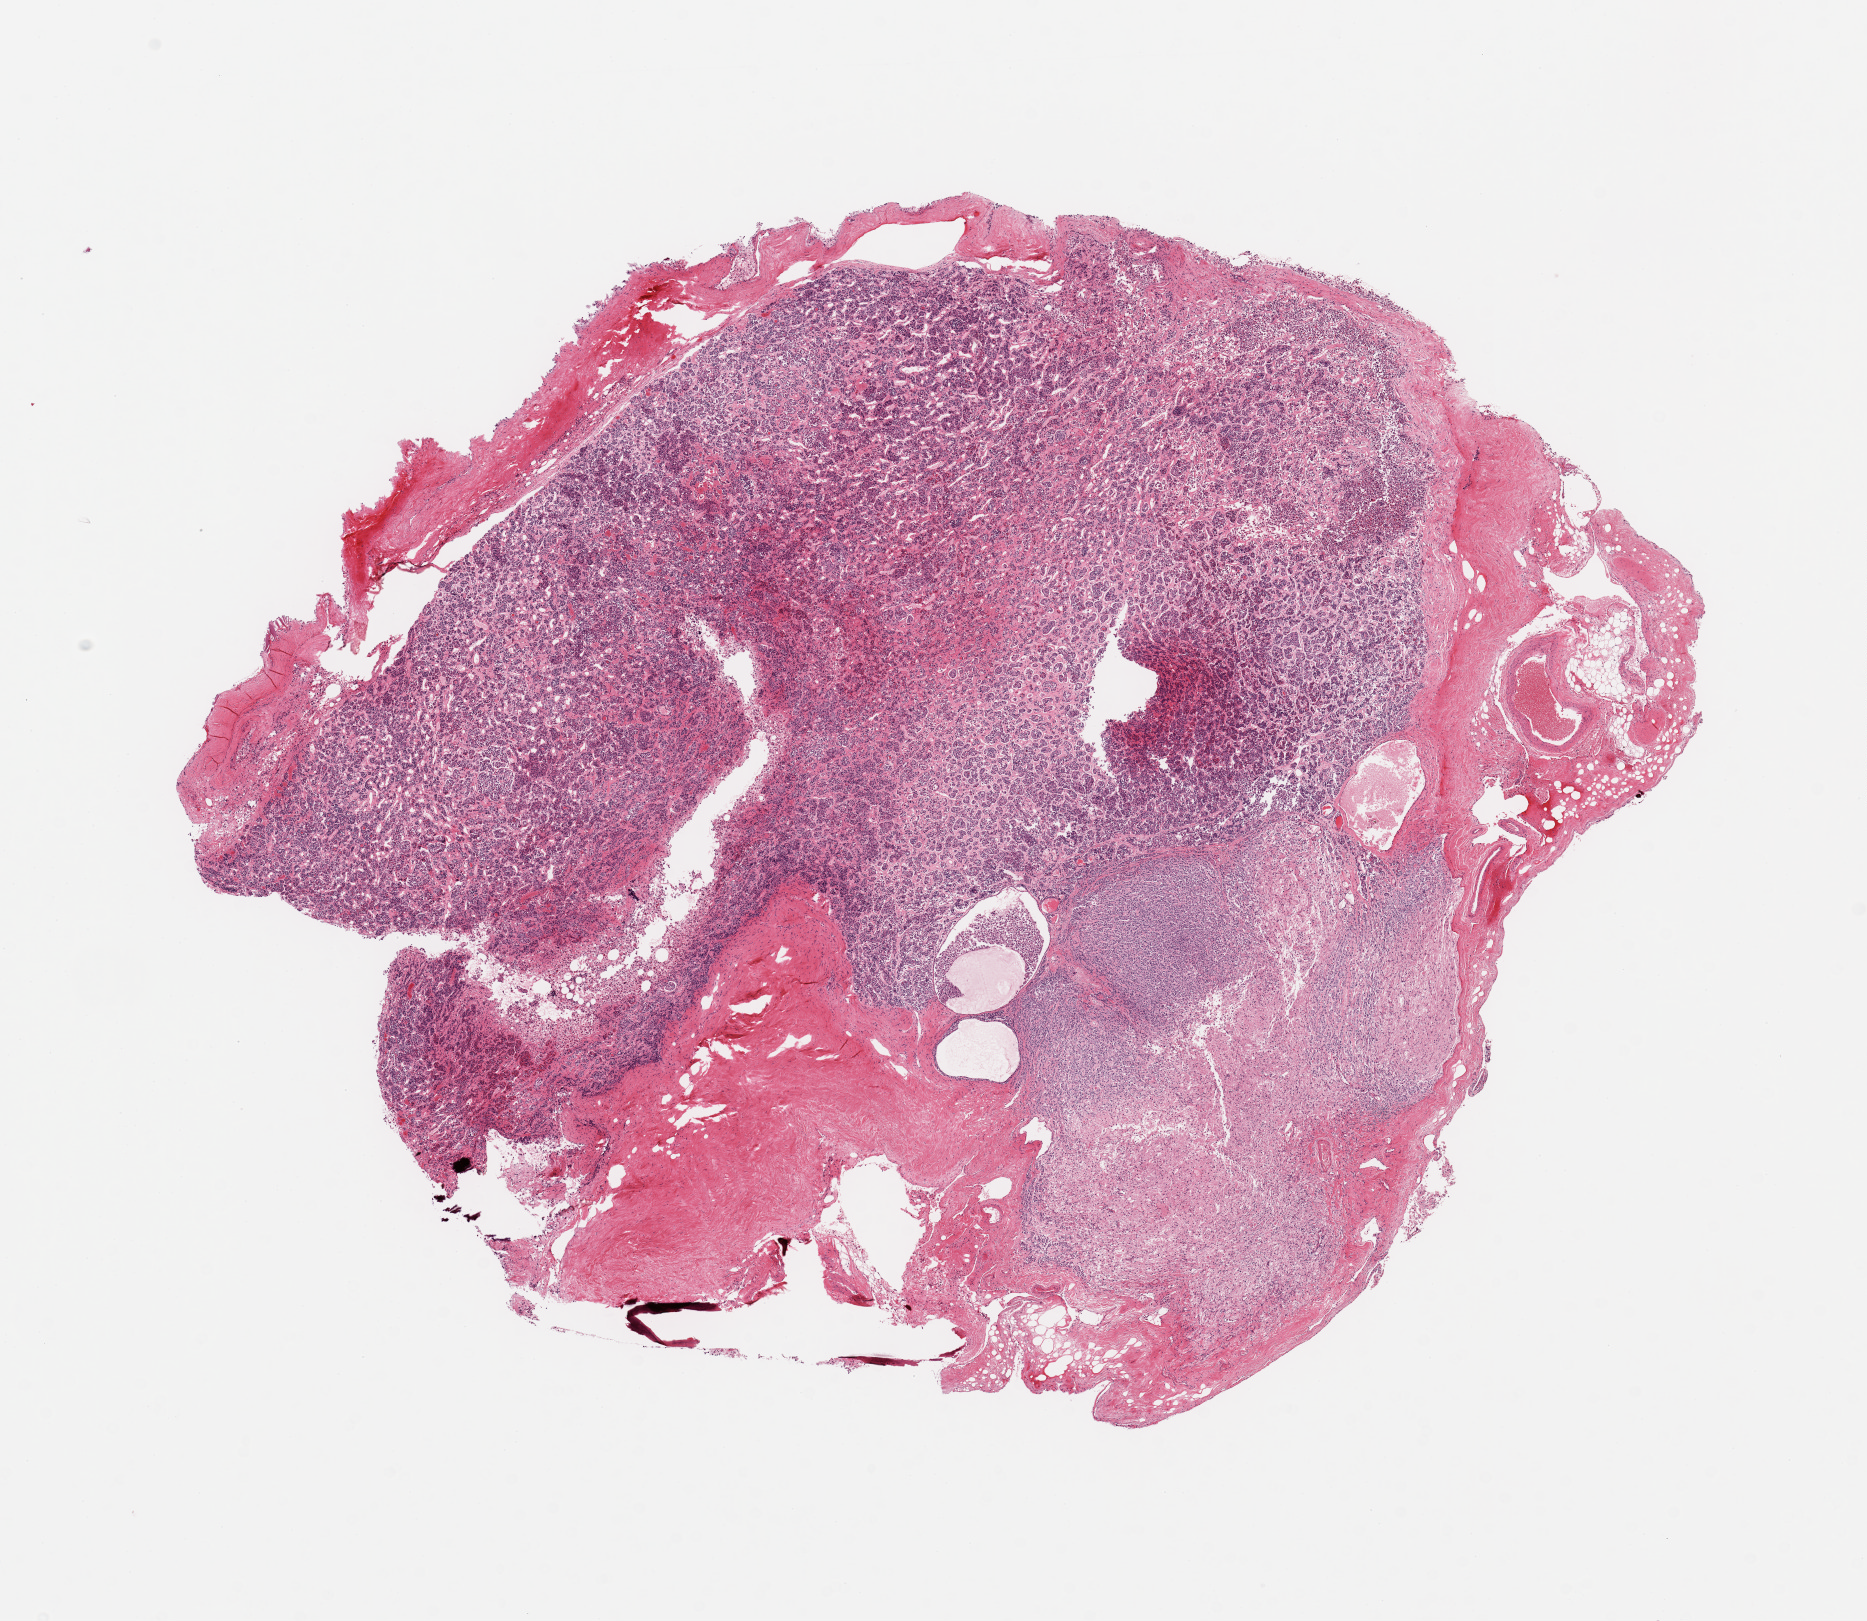
Haematoxylin and eosin whole-slide image, brightfield — low-resolution overview of the scanned area, about 14.8 x 12.8 mm (slide scanned at 20x), PAXgene-fixed, paraffin-embedded tissue, sampled site (target tissue): pituitary, donor tissue sample. Donor: male.
• pathologist's review note for this sample: 1 piece, partially shows moderate autolysis; mainly adenohypophysis with focal (~3mm) neurohypophysis